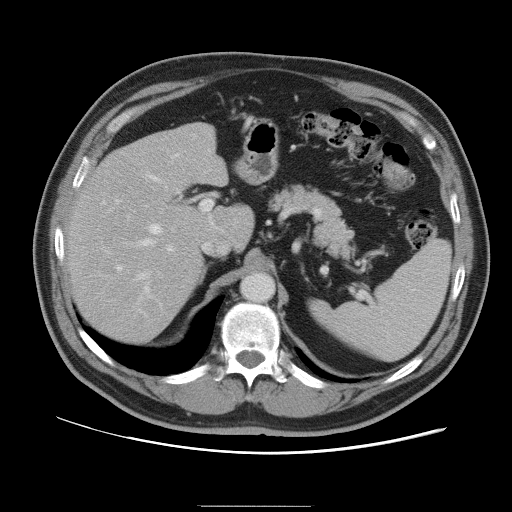
Contrast-enhanced abdominal CT, one axial slice; intravenous contrast given; soft-tissue window (W 400 / L 40 HU); 5 mm slice thickness; 512 × 512 image matrix, field of view 399 × 399 mm. Male patient, age 64 years. From the clinical record (not read from this slice): diagnosis: colorectal cancer liver metastases, imaged before liver resection; multiple liver metastases: yes; largest metastasis: 3 cm; disease in both lobes: yes.
Annotated regions visible in this slice (outlined manually by an expert reader):
- hepatic veins: bounding box (x1, y1, x2, y2) in pixels: (139, 176, 162, 279)
- liver: (68, 124, 254, 343)
- planned liver remnant (the part of the liver to remain after resection): (68, 137, 253, 344)
- portal vein (with intrahepatic branches): (116, 200, 213, 271)